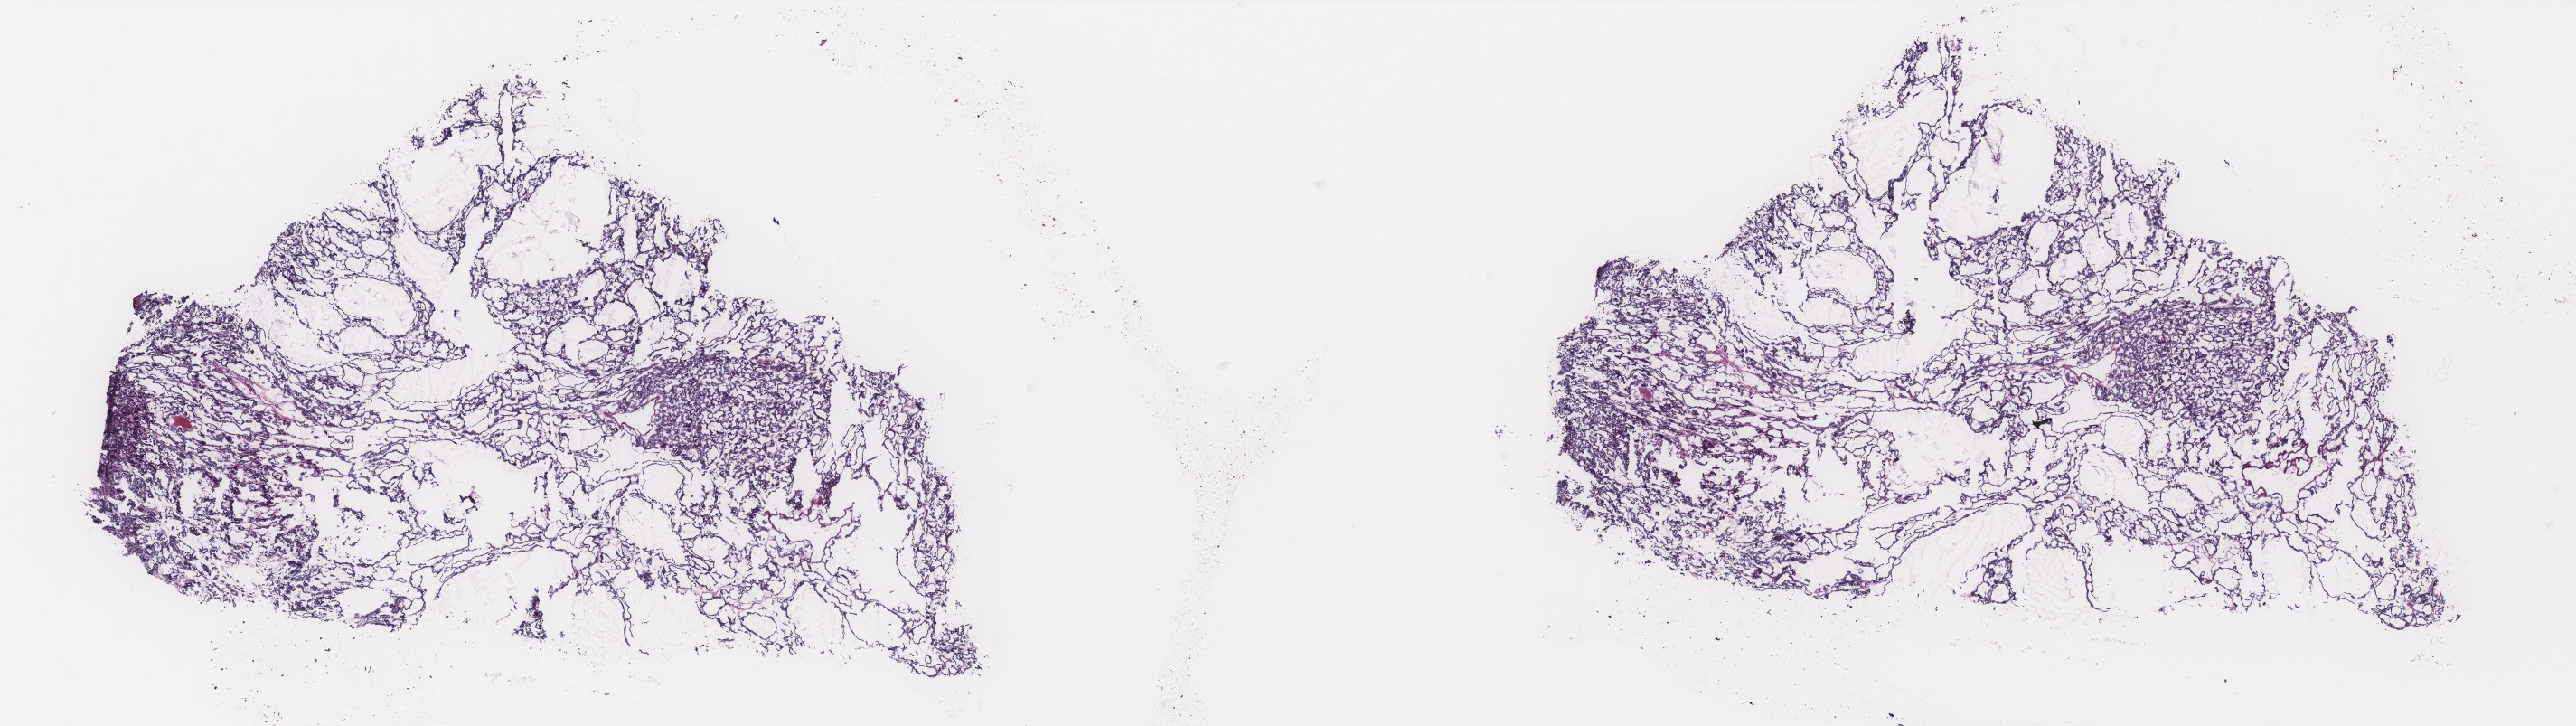
Digitized H&E-stained tissue section (whole slide) — shown as a low-resolution overview of the whole scanned area (about 22.8 x 6.4 mm, from a 40x scan); frozen section from the bottom of the tissue portion; primary tumour sample from the thyroid. Male patient; age at initial diagnosis 55 years. Slide review estimates, as recorded: tumour cells 100%, tumour nuclei 98%, normal cells 0%, stromal cells 0%, necrosis 0%. Infiltration values recorded for this section: lymphocyte infiltration 0%, monocyte infiltration 0%, neutrophil infiltration 0%.
- histologic diagnosis: Papillary adenocarcinoma, NOS (thyroid gland)
- AJCC pathologic stage: II
- lymph nodes positive (case pathology): 0 of 5 examined